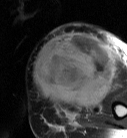
MRI of an extremity soft-tissue mass, one axial slice; position 25 of 87 along the scan axis; T2-weighted fat-saturated; MR volume resampled by the dataset authors to the PET/CT grid (not the native acquisition matrix); 127 × 138 image matrix. Female patient. Case-level facts recorded for this patient, not image findings: histological type: pleiomorphic leiomyosarcoma; grade: high; site of the primary tumour: left biceps.
Annotated regions visible in this slice (expert contour drawn on MRI and transferred to this co-registered scan by the dataset authors):
- gross tumour volume including surrounding oedema: box from (x=34, y=32) to (x=115, y=108) px
- gross tumour volume (mass): (x=34, y=32)–(x=115, y=108)